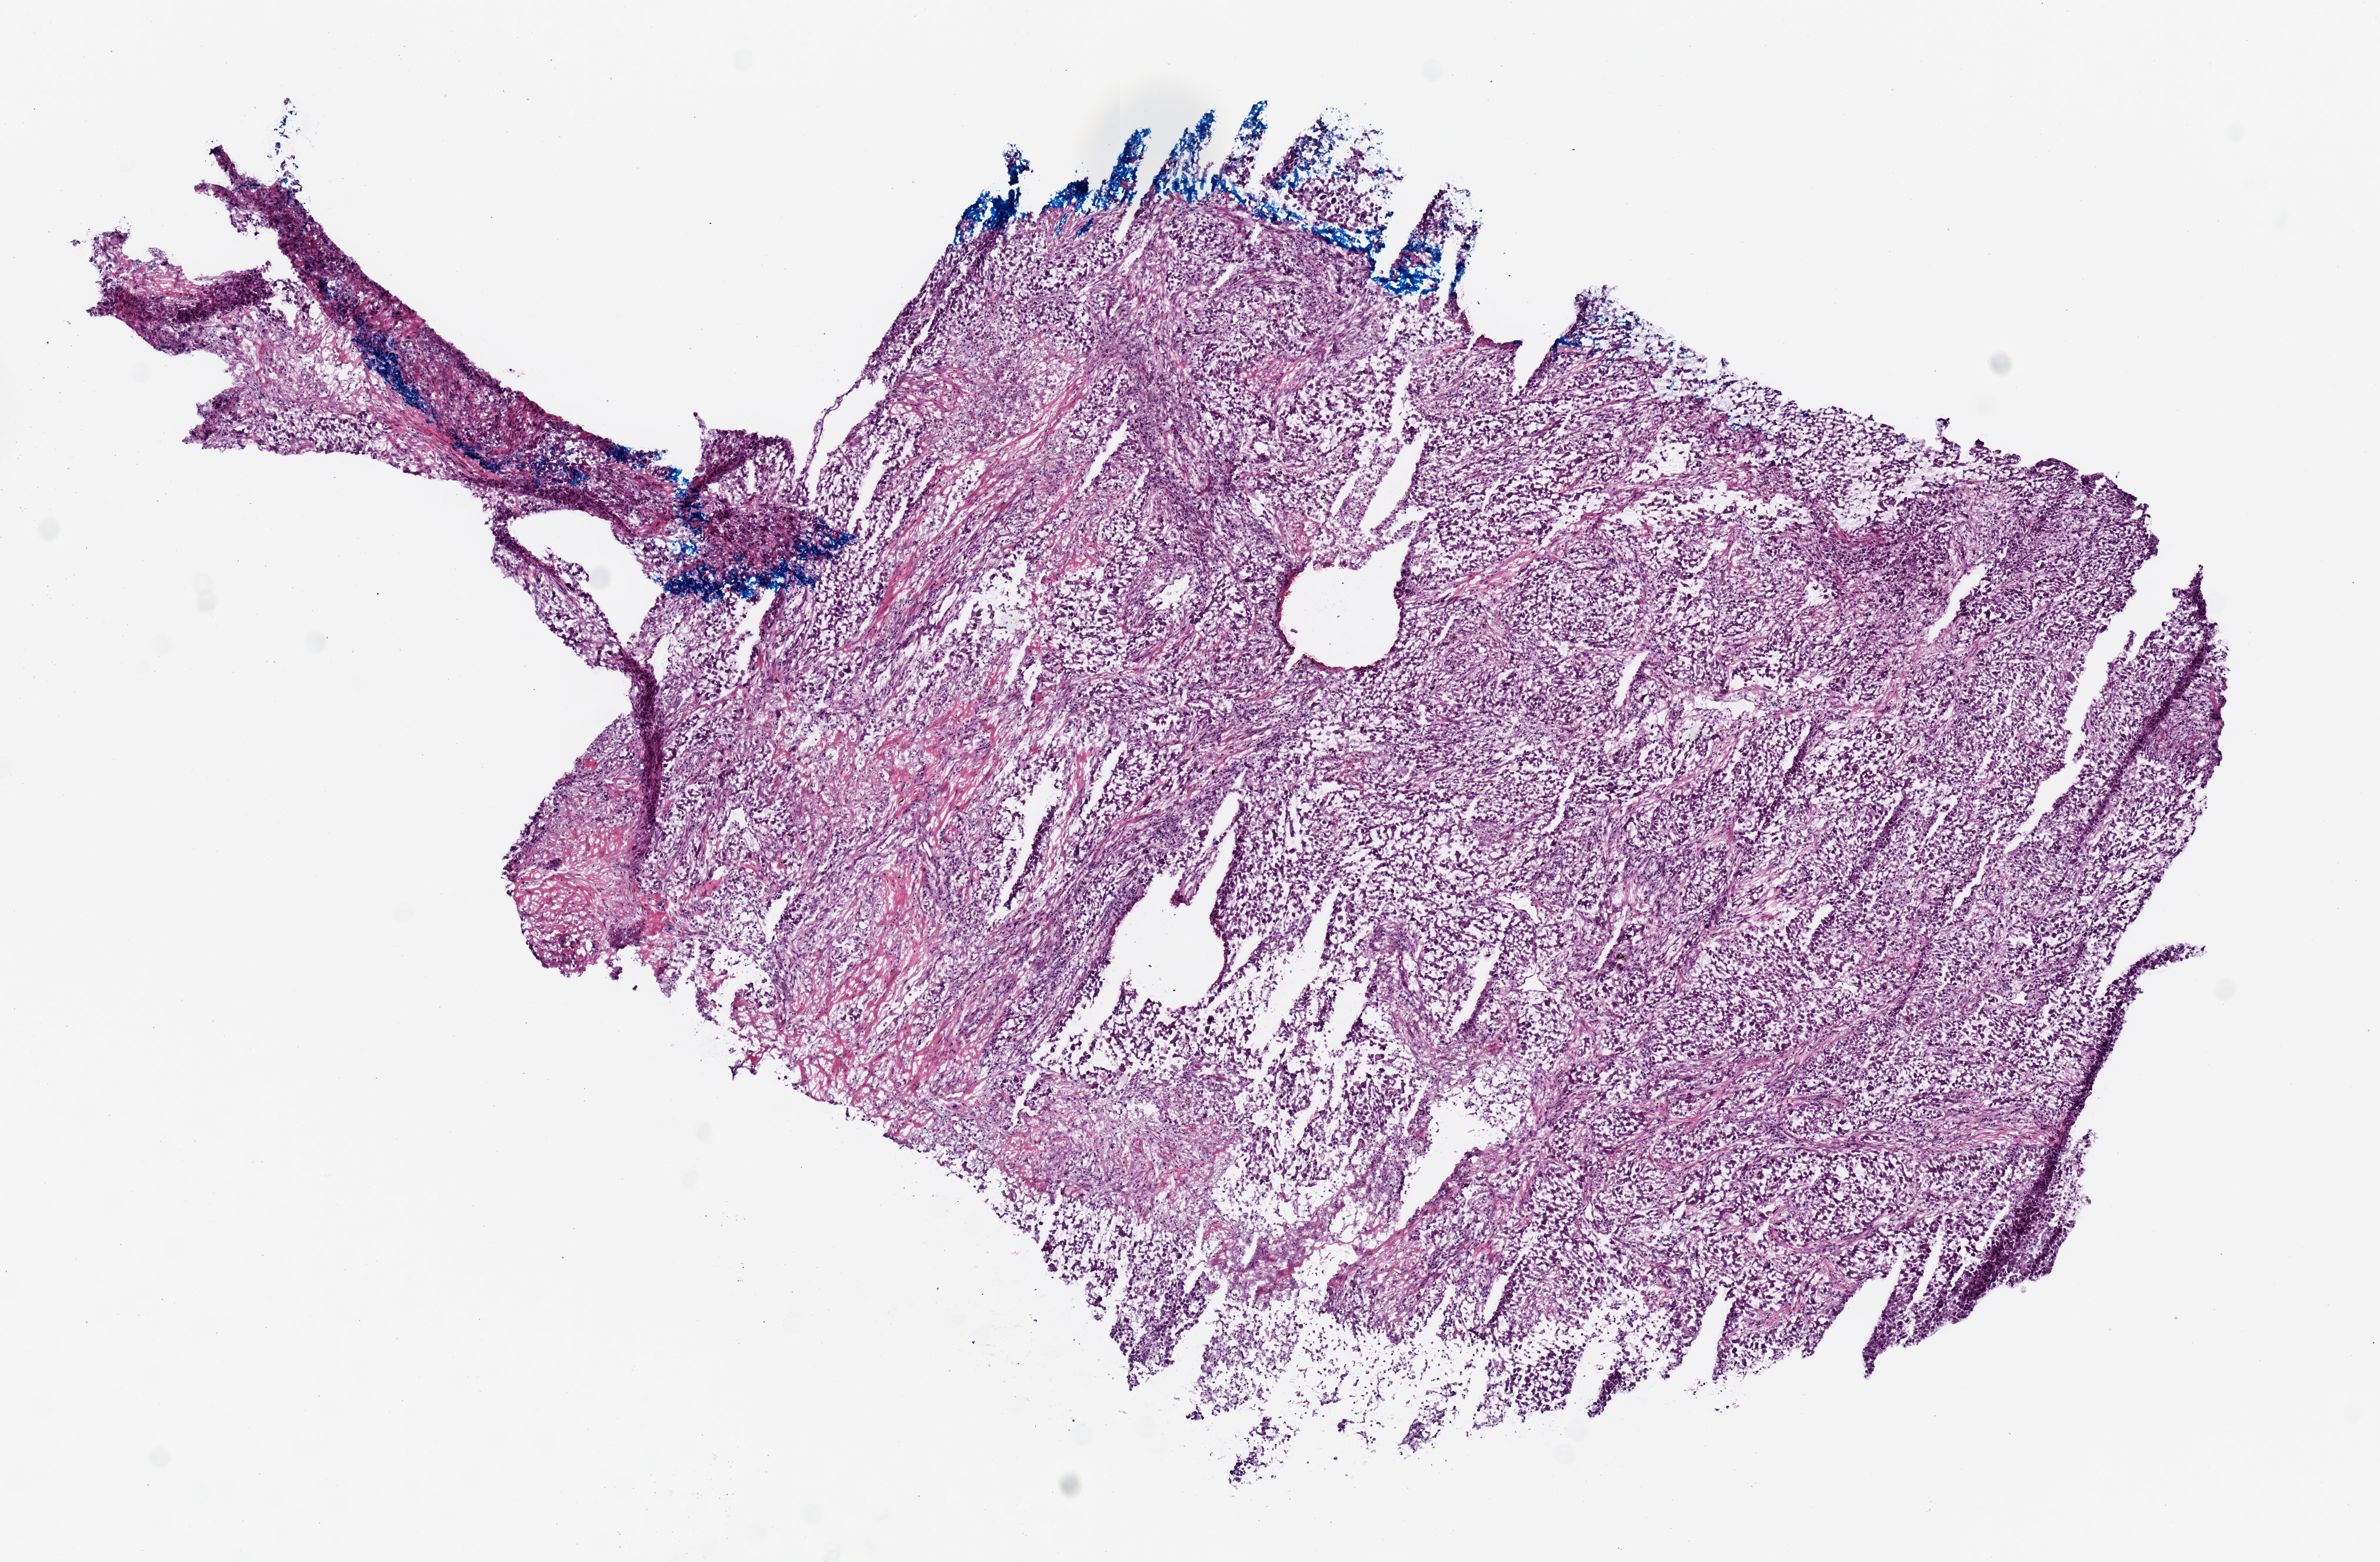
Digitized Hematoxylin and eosin (H&E) stained tissue section (whole slide), a low-resolution overview of the entire scanned area, about 8.0 x 5.3 mm (acquisition: 20x scan), frozen section from the top of the tissue portion, sample: primary tumour, lung. Female, age 62 years at initial diagnosis. Slide review estimates, as recorded: tumour cells 85%, tumour nuclei 80%, normal cells 0%, stromal cells 10%, necrosis 5%.
- histologic diagnosis: Adenocarcinoma, NOS (upper lobe, lung)
- laterality: right
- AJCC pathologic stage: IIB (7th edition)